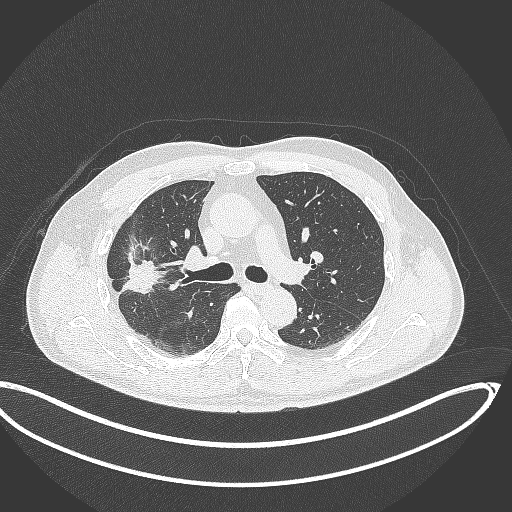
Chest CT, one axial slice. Slice 216 of 391 in the series (ordered by position). Reconstruction kernel B70f. 120 kVp. Lung window (W 1500 / L -600 HU). 512 × 512 image matrix, field of view 439 × 439 mm. Patient: male, 63 years. Case-level facts recorded for this patient, not image findings: clinical TNM (as recorded): T1c N0 M0.
Structures marked on this image (bounding box drawn by a radiologist):
- lung tumour (recorded histology: adenocarcinoma): bounding box (x1, y1, x2, y2) in pixels: (119, 246, 163, 302)